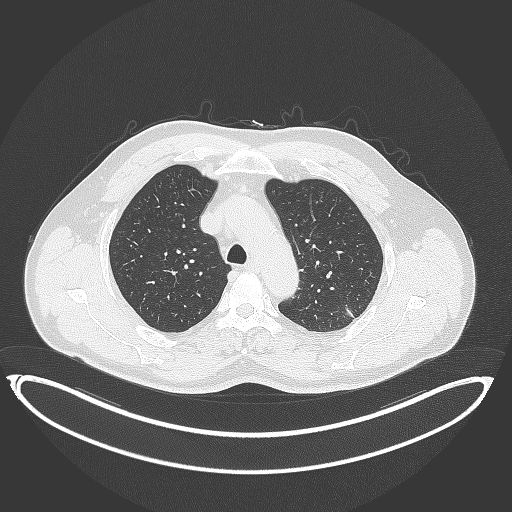
Chest CT, one axial slice; position 277 of 399 along the scan axis; reconstruction kernel B70f; lung window (W 1500 / L -600 HU); 1 mm slice thickness; 512 × 512 image matrix, field of view 469 × 469 mm. Male patient, age 58 years. From the clinical record (not read from this slice): clinical TNM (as recorded): T1c N0 M0; histopathological grade: G1-2.
Structures marked on this image (rectangle marked by the reading radiologist):
- lung tumour (recorded histology: adenocarcinoma): box from (x=340, y=300) to (x=364, y=327) px